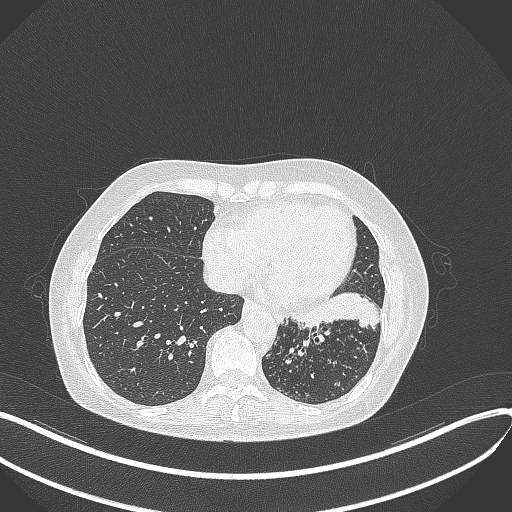
Chest CT, one axial slice; 100 kVp; lung window (W 1500 / L -600 HU); 1 mm slice thickness; 512 × 512 image matrix, field of view 400 × 400 mm. Patient: female, 63 years. From the clinical record (not read from this slice): clinical TNM (as recorded): T1b N0 M0; histopathological grade: G2-3.
Outlined on this slice (bounding box drawn by a radiologist):
- lung tumour (recorded histology: adenocarcinoma): bounding box <290,291,379,334> (left, top, right, bottom; pixels)